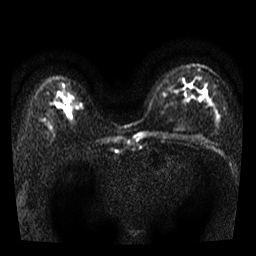
Breast MRI, one axial slice. Diffusion-weighted series; image 2 of 4 stored at this slice position (different b-values; order by instance number). 3 T. 5 mm slice thickness. 256 × 256 image matrix. Female patient.
Structures marked on this image (outlined manually by an expert reader):
- tumour on diffusion-weighted imaging: bounding box [x1, y1, x2, y2] px = [56, 97, 69, 110]